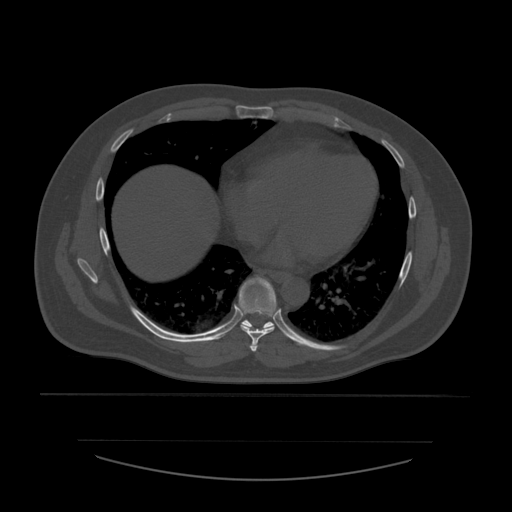
CT including the spine, one axial slice. Slice 351 of 532 in the series (ordered by position). Reconstruction kernel STANDARD. 120 kVp. Bone window (W 1800 / L 400 HU). 512 × 512 image matrix, field of view 441 × 441 mm. Patient age 44 years. From the clinical record (not read from this slice): primary cancer: soft tissue sarcoma.
Annotated regions visible in this slice (semi-automatic segmentation, software-assisted and operator-edited):
- T6 vertebra: bounding box <250,342,258,353> (left, top, right, bottom; pixels)
- T7 vertebra: <239,277,277,344>
- T8 vertebra: <242,280,277,332>